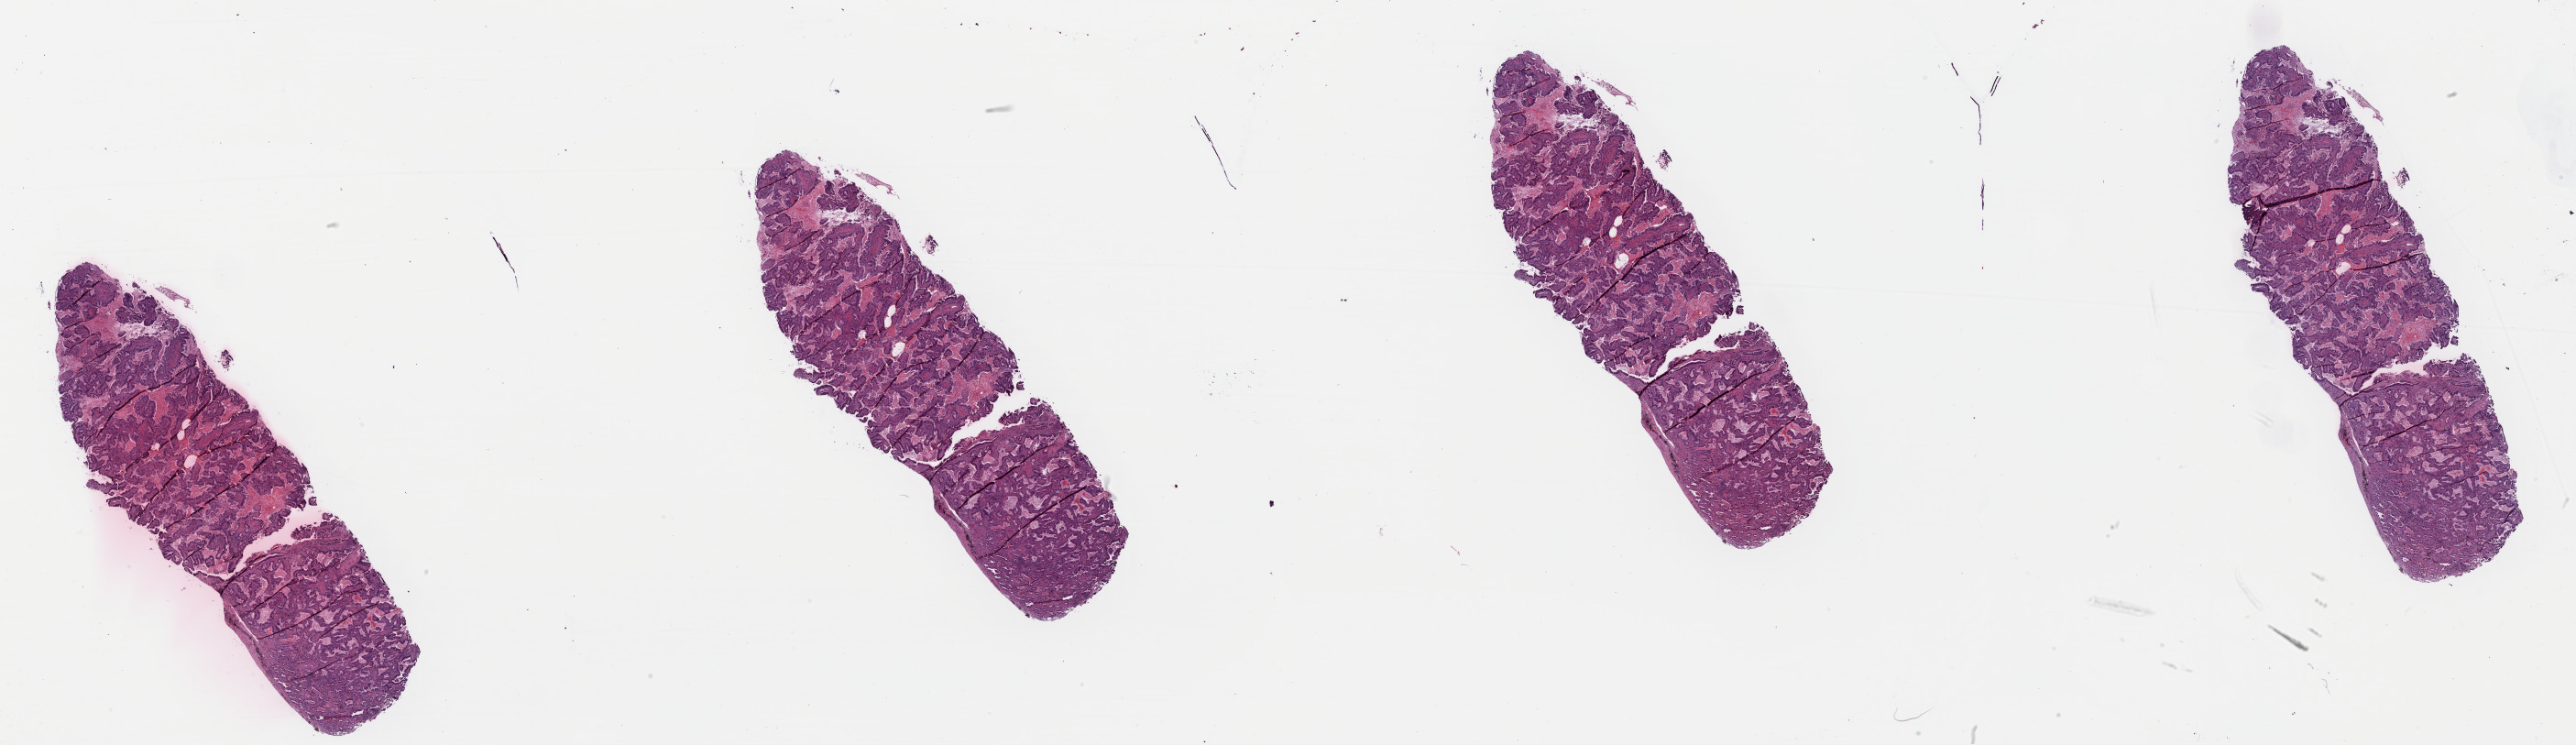
Whole-slide histology image, H&E-stained — a low-resolution overview of the entire scanned area, about 44.4 x 12.8 mm (slide scanned at 40x), formalin-fixed paraffin-embedded (FFPE) diagnostic section, lung, primary tumour sample. Female, age 67 years at initial diagnosis.
AJCC pathologic stage: IA. Laterality: right. Histologic diagnosis: Adenocarcinoma, NOS (lower lobe, lung).